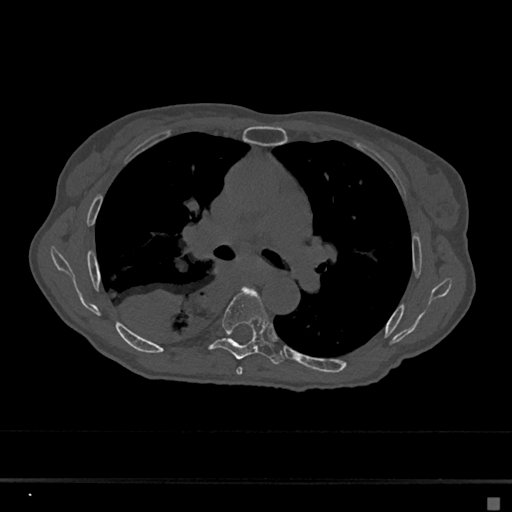
CT including the spine, one axial slice; slice 423 of 797 in the series (ordered by position); bone window (W 1800 / L 400 HU); 0.5 mm slice thickness; 512 × 512 image matrix, field of view 360 × 360 mm. Female patient, age 68 years. Case-level facts recorded for this patient, not image findings: primary cancer: renal.
Structures marked on this image (semi-automatically segmented with operator editing):
- T5 vertebra: bounding box [x1, y1, x2, y2] px = [236, 287, 258, 375]
- T6 vertebra: [209, 286, 284, 364]